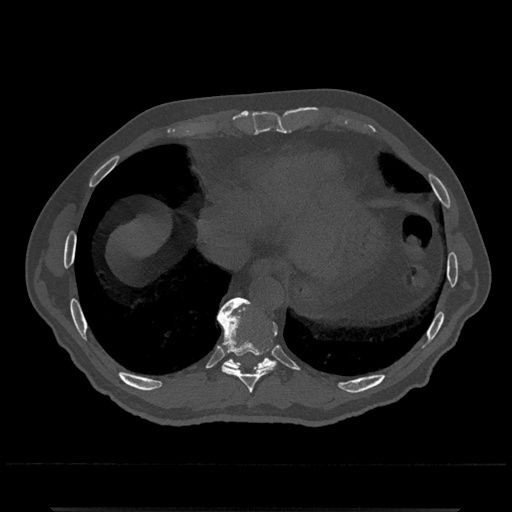
CT including the spine, one axial slice; slice 592 of 797 in the series (ordered by position); reconstruction kernel Br40s/3; 120 kVp; bone window (W 1800 / L 400 HU); 0.5 mm slice thickness; 512 × 512 image matrix, field of view 393 × 393 mm. Male patient, age 67 years. From the clinical record (not read from this slice): primary cancer: prostate.
Structures marked on this image (semi-automatic segmentation, software-assisted and operator-edited):
- T10 vertebra: bounding box <218,297,276,370> (left, top, right, bottom; pixels)
- T9 vertebra: <217,300,278,393>